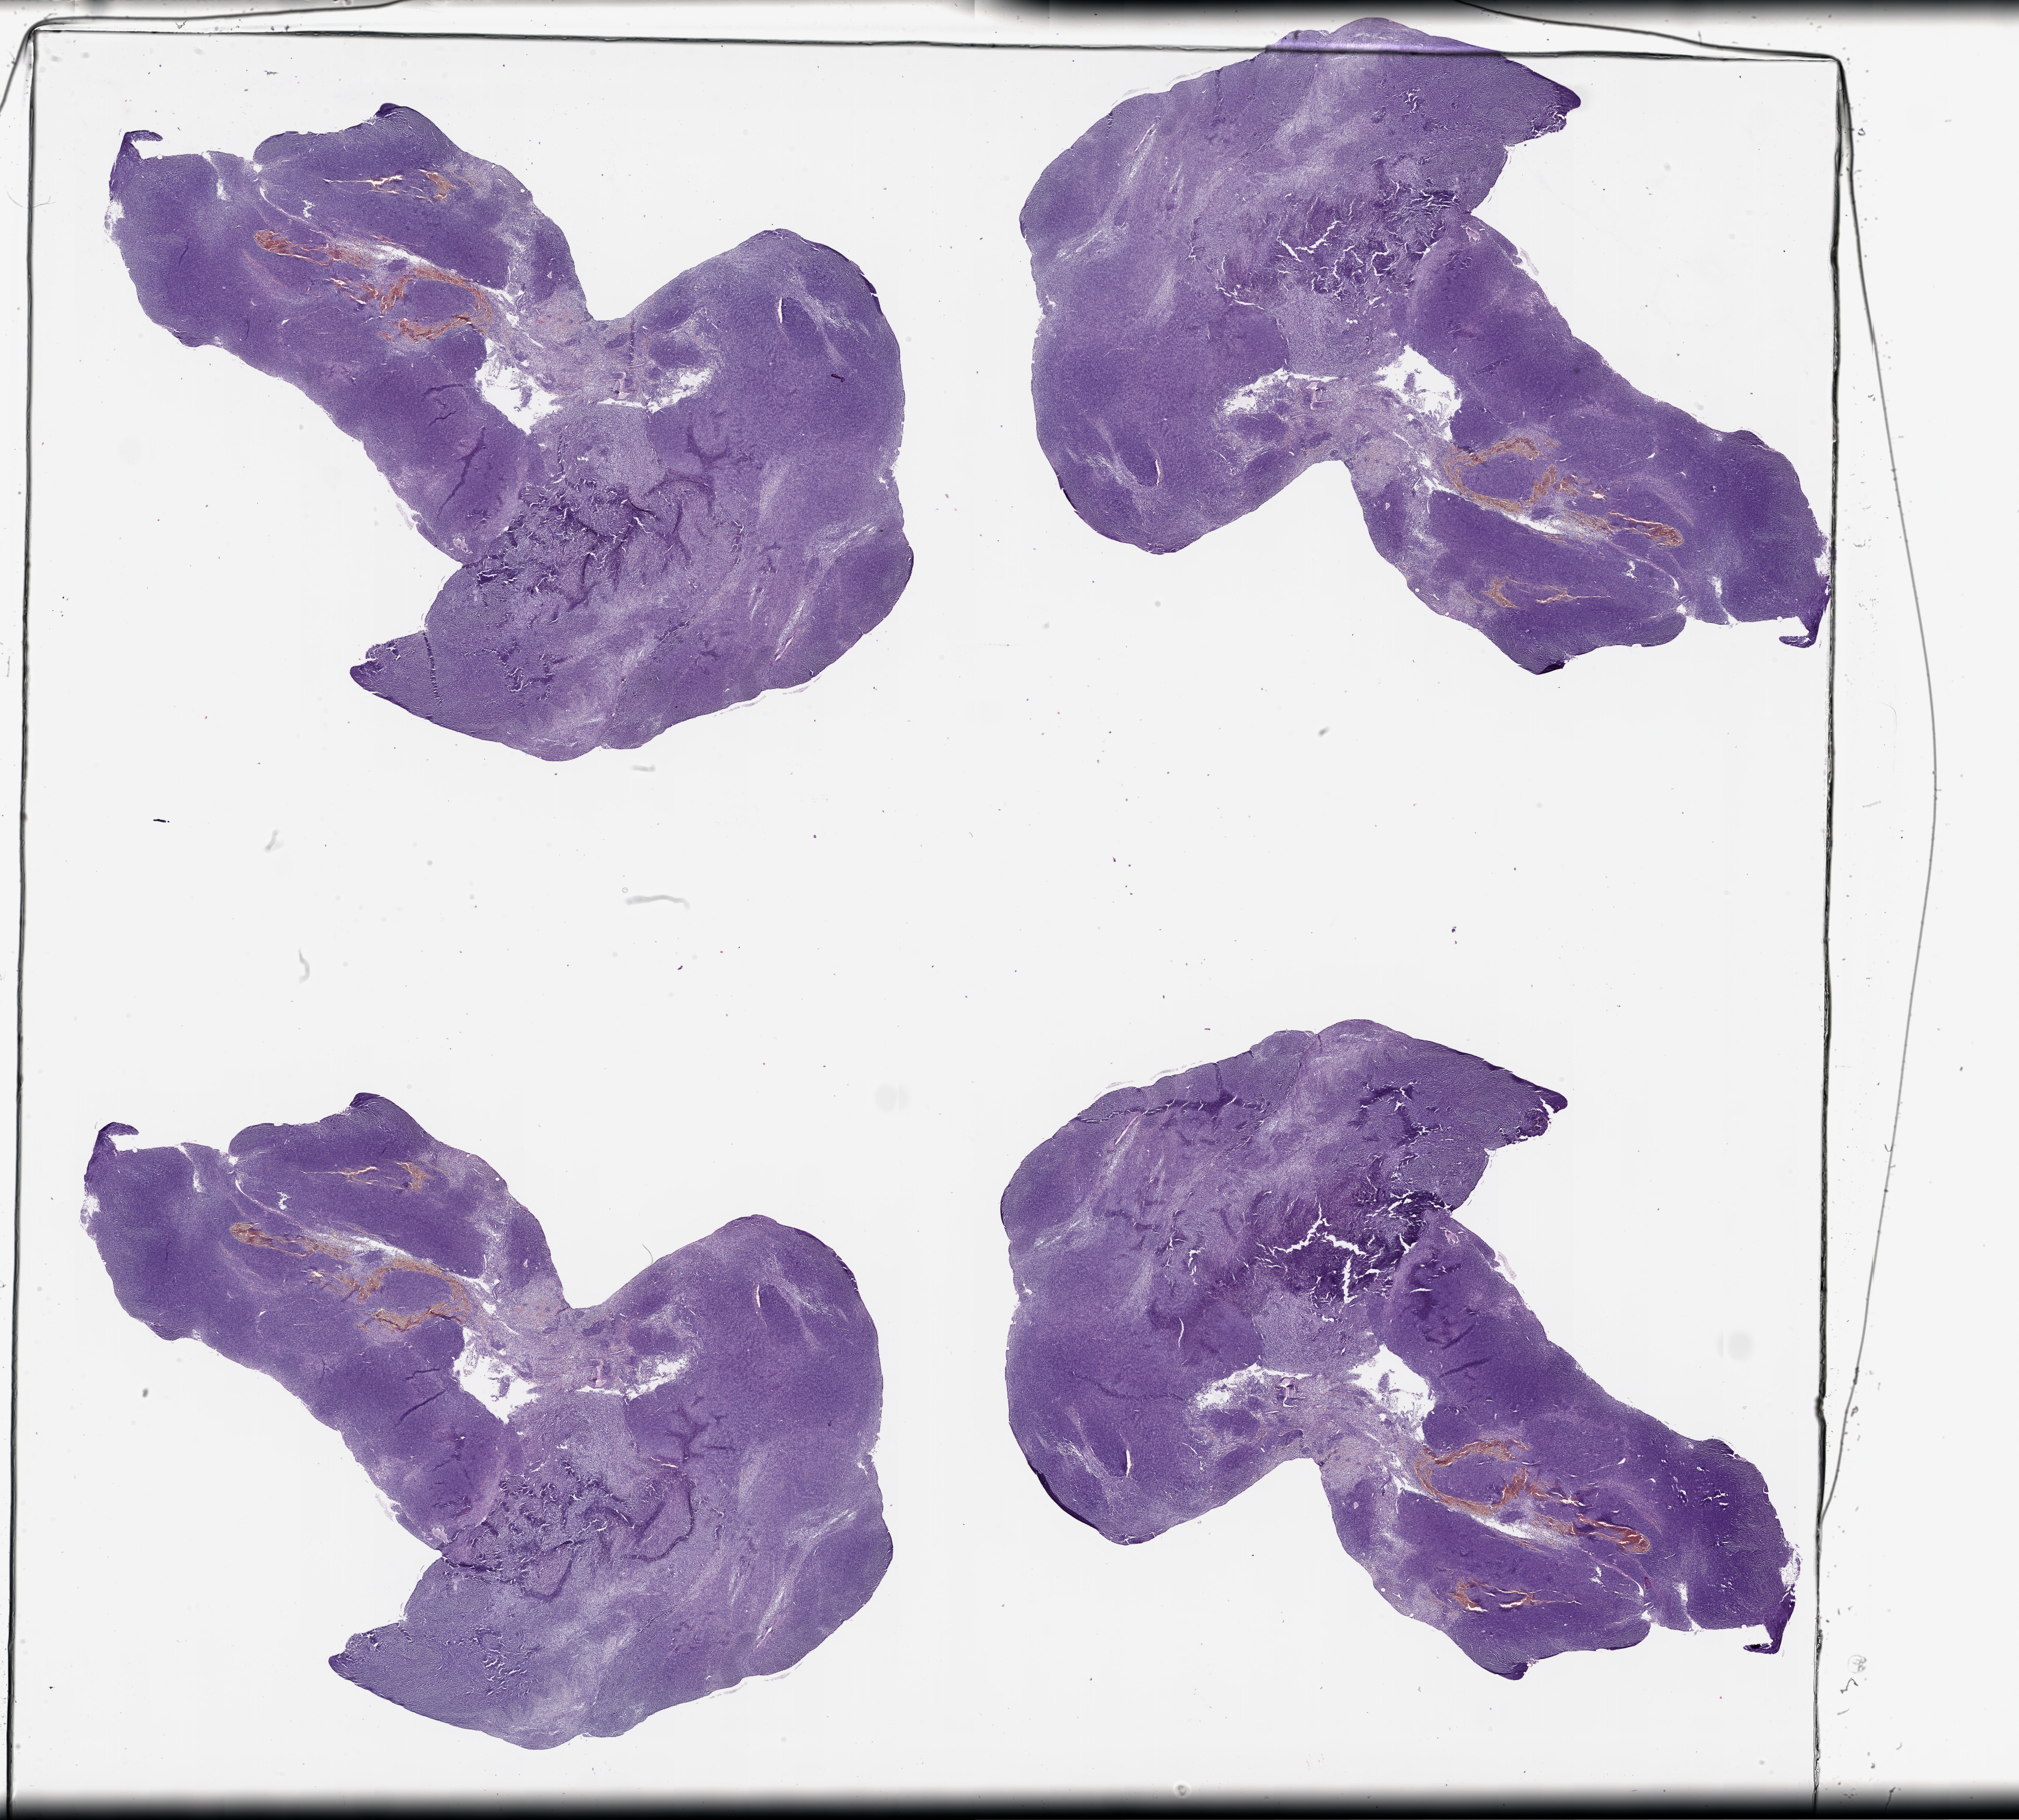
H&E whole-slide image — shown as a low-resolution overview of the whole scanned area (about 27.1 x 24.4 mm).
Patient diagnosis (cohort enrolment): sarcoma (site not recorded at cohort level).